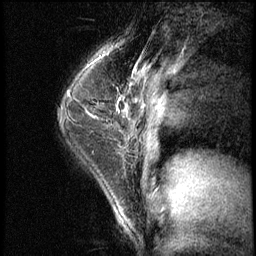
Breast MRI (dynamic contrast-enhanced), one sagittal slice; slice 43 of 62 in the series (ordered by position); 3 images stored at this slice position (order not interpretable as contrast timing); 1.5 T; TE 4.2 ms, TR 8.7 ms; 256 × 256 image matrix. Female patient, age 35 years. From the clinical record (not read from this slice): setting: breast cancer imaged before/during neoadjuvant chemotherapy; receptor status: HER2-positive.
Annotated regions visible in this slice (semi-automatically segmented with operator editing):
- analysis volume of interest (the breast-tissue region the enhancement analysis was run in; not a lesion): bounding box [x1, y1, x2, y2] px = [71, 78, 120, 139]
- tumour enhancement mask (voxels above the 140 % enhancement threshold inside the analysis volume of interest): [94, 99, 120, 118]